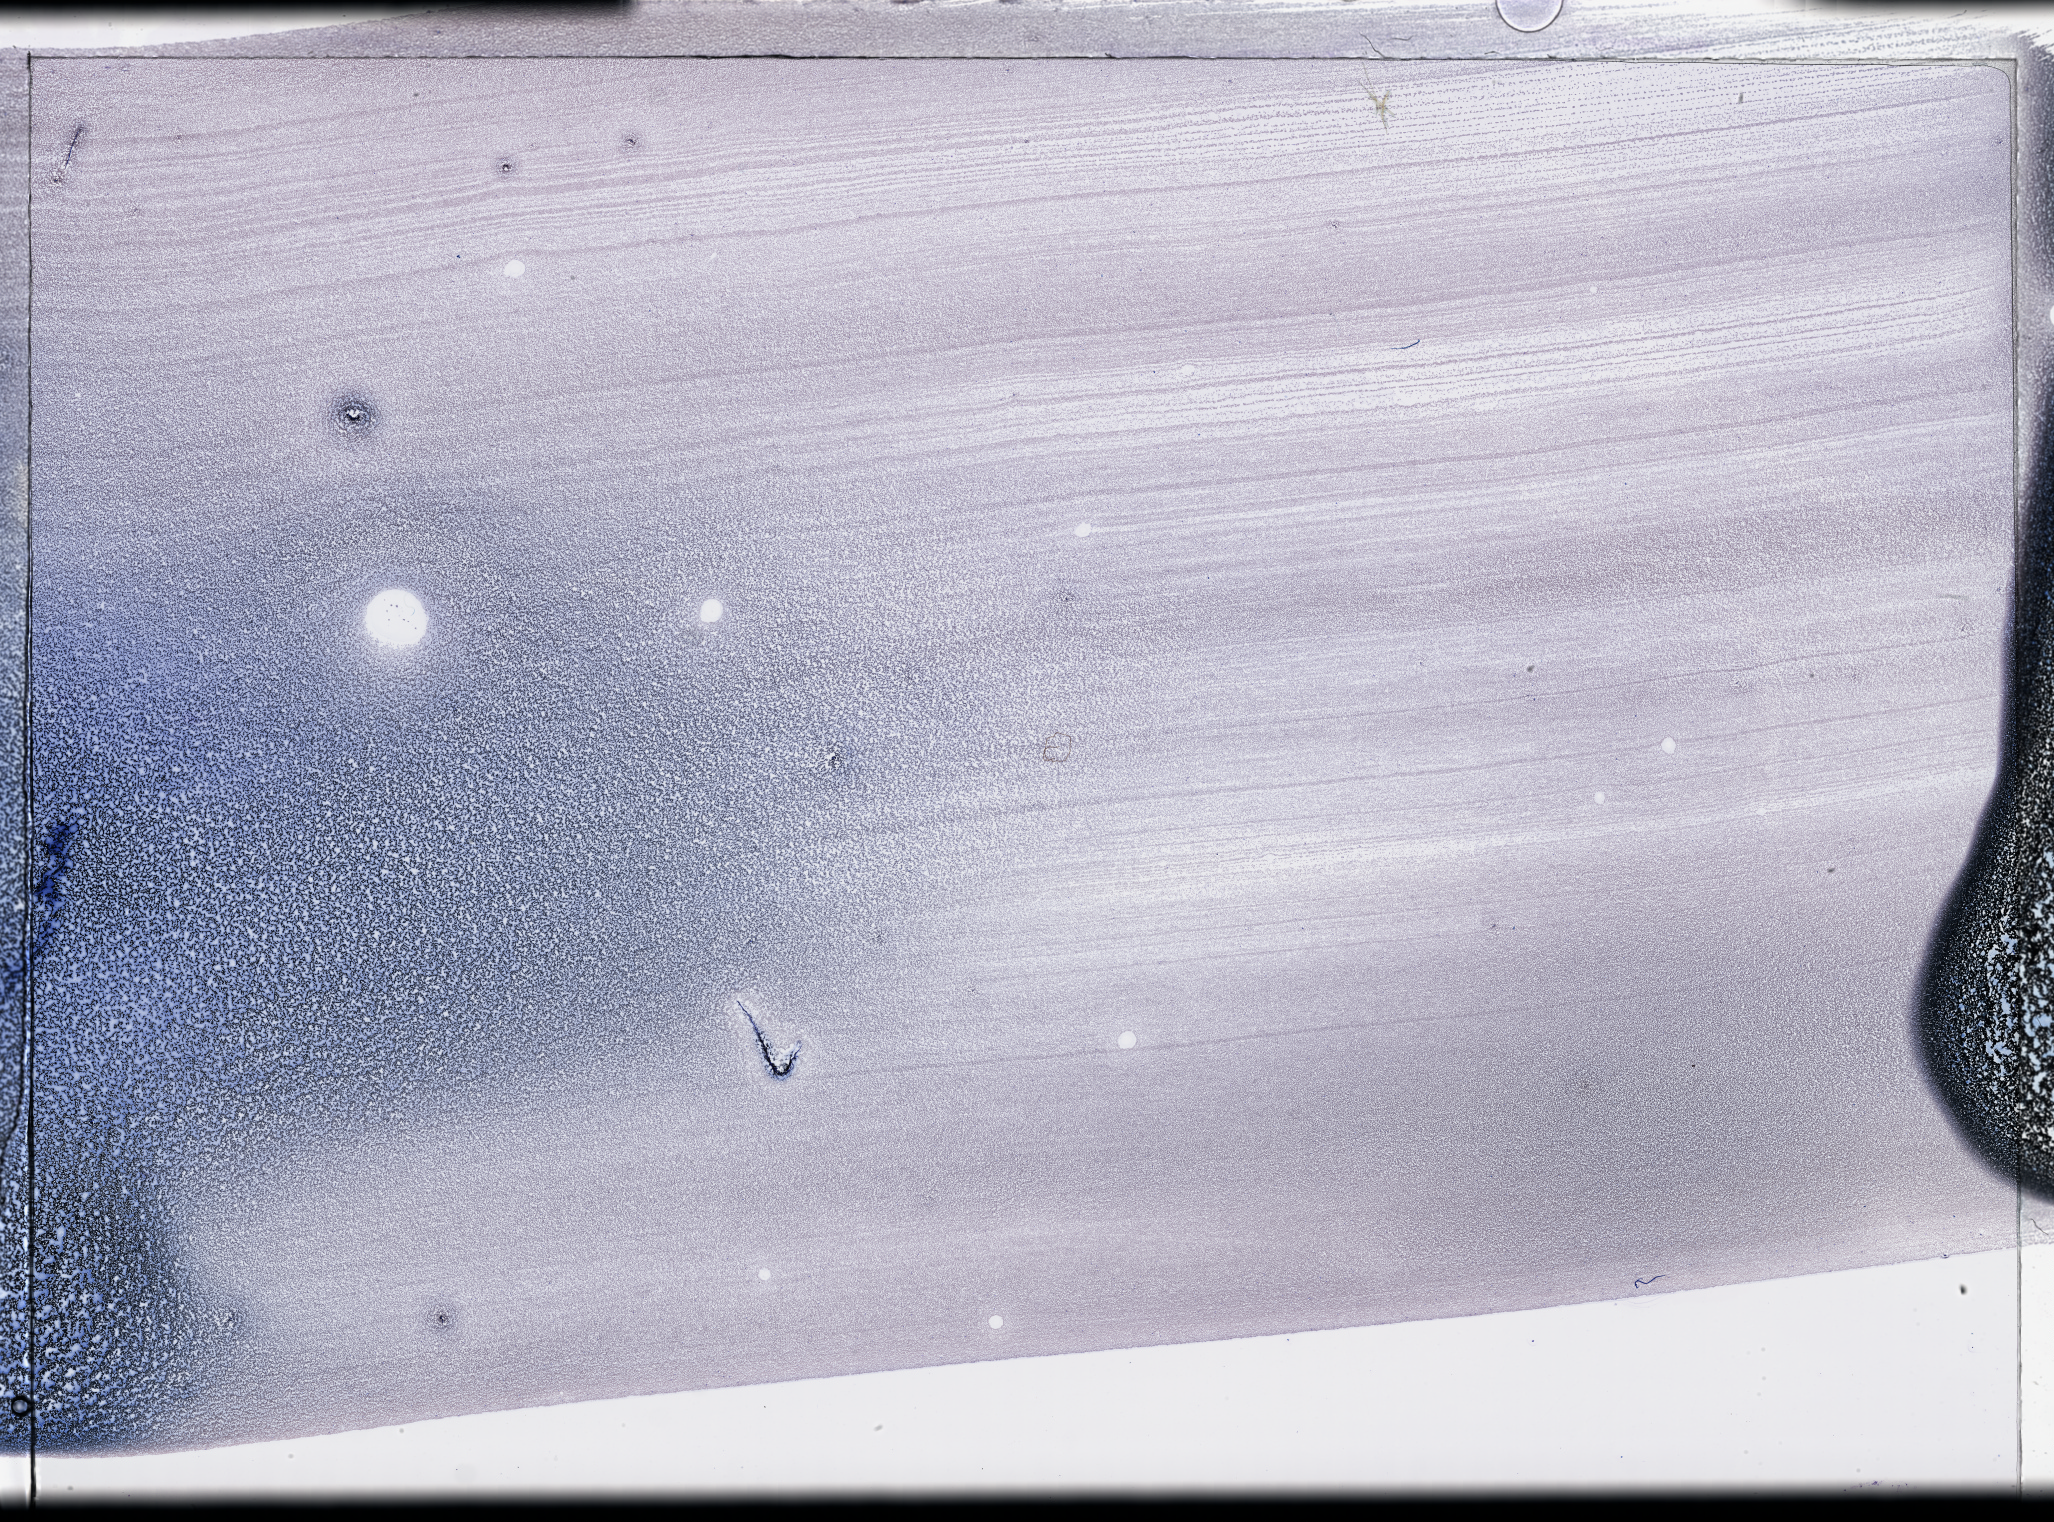
H&E whole-slide image, a low-resolution overview of the entire scanned area, about 33.2 x 24.6 mm, peripheral blood (leukaemic) sample. Female, 45 y/o.
Diagnosis: Acute Myeloid Leukemia.